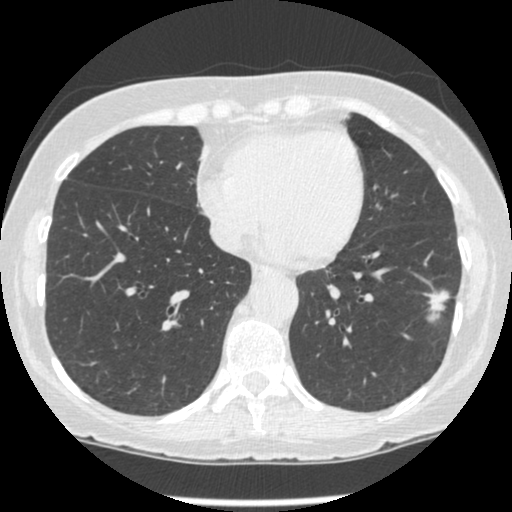
Low-dose screening chest CT, one axial slice; position 87 of 247 along the scan axis; 120 kVp; lung window (W 1500 / L -600 HU); 1.25 mm slice thickness; 512 × 512 image matrix, field of view 303 × 303 mm.
Annotated regions visible in this slice (outlined manually by an expert reader):
- lesion 1 (tumor, lower lobe of left lung): bounding box (x1, y1, x2, y2) in pixels: (425, 291, 450, 322)